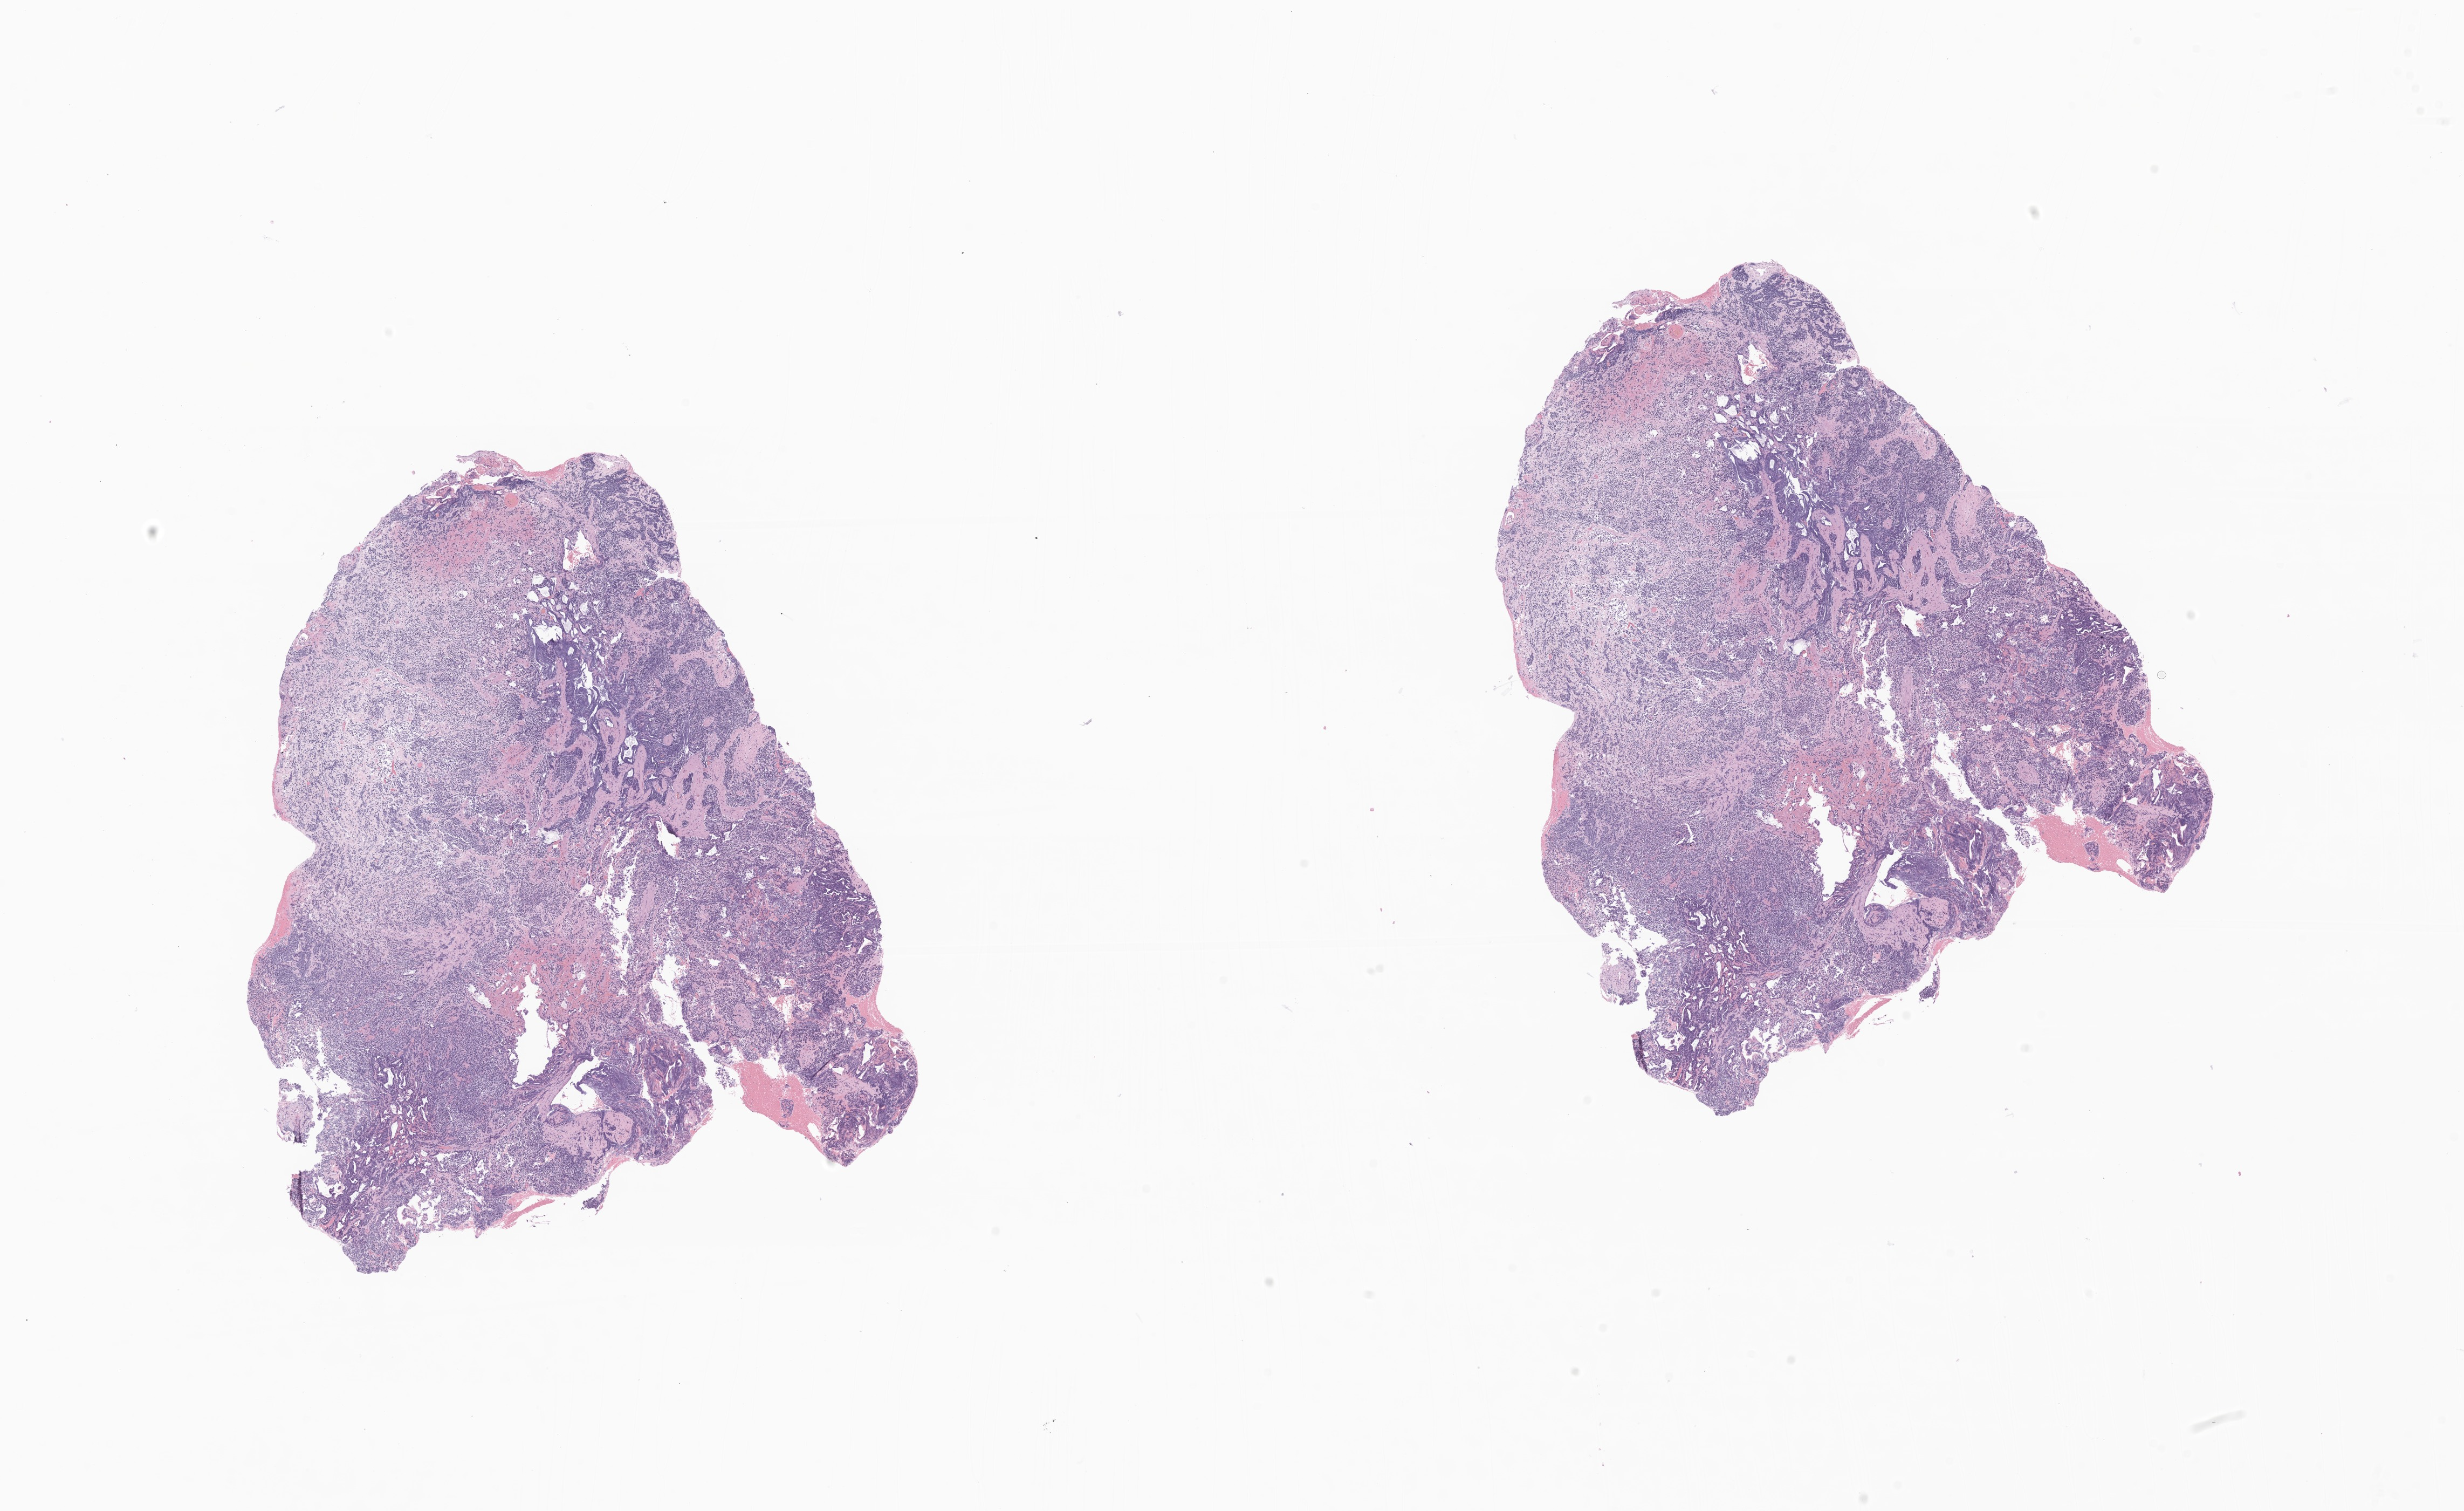
H&E whole-slide image of tumor tissue from the temporal lobe, whole scanned area (about 19.3 x 11.8 mm) shown as a low-resolution overview; formalin-fixed paraffin-embedded section. Female patient, age 42 months.
• diagnosis: Tumor cells, malignant